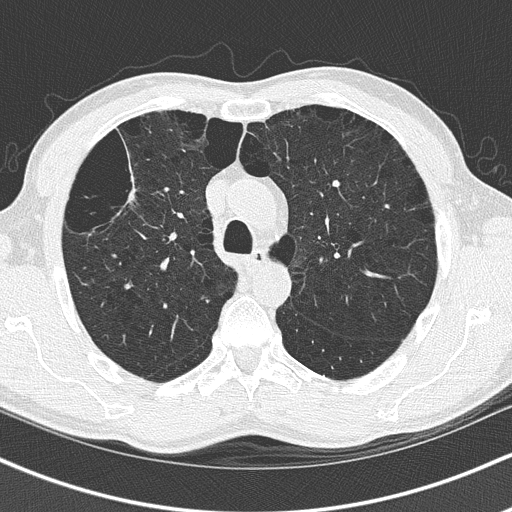
Axial slice from a low-dose chest CT screening exam, first (baseline) screen, lung window (W 1500 / L -600 HU), lung (sharp) reconstruction kernel (B50f), 120 kVp, slice 57 of 168 in the series. Male, age 66 years at enrolment. Current smoker at enrolment.
Expert reader's lesion annotation, box from (x=104, y=169) to (x=155, y=221) px. The screening reader recorded 3 non-calcified nodules or masses ≥4 mm on this exam; which of them this box marks is not recorded. Later outcome: lung cancer diagnosed 978 days after this screen — squamous cell carcinoma, adenoid, right upper lobe, poorly differentiated (G3), stage IIB (AJCC 6th edition), 50 mm at pathology.